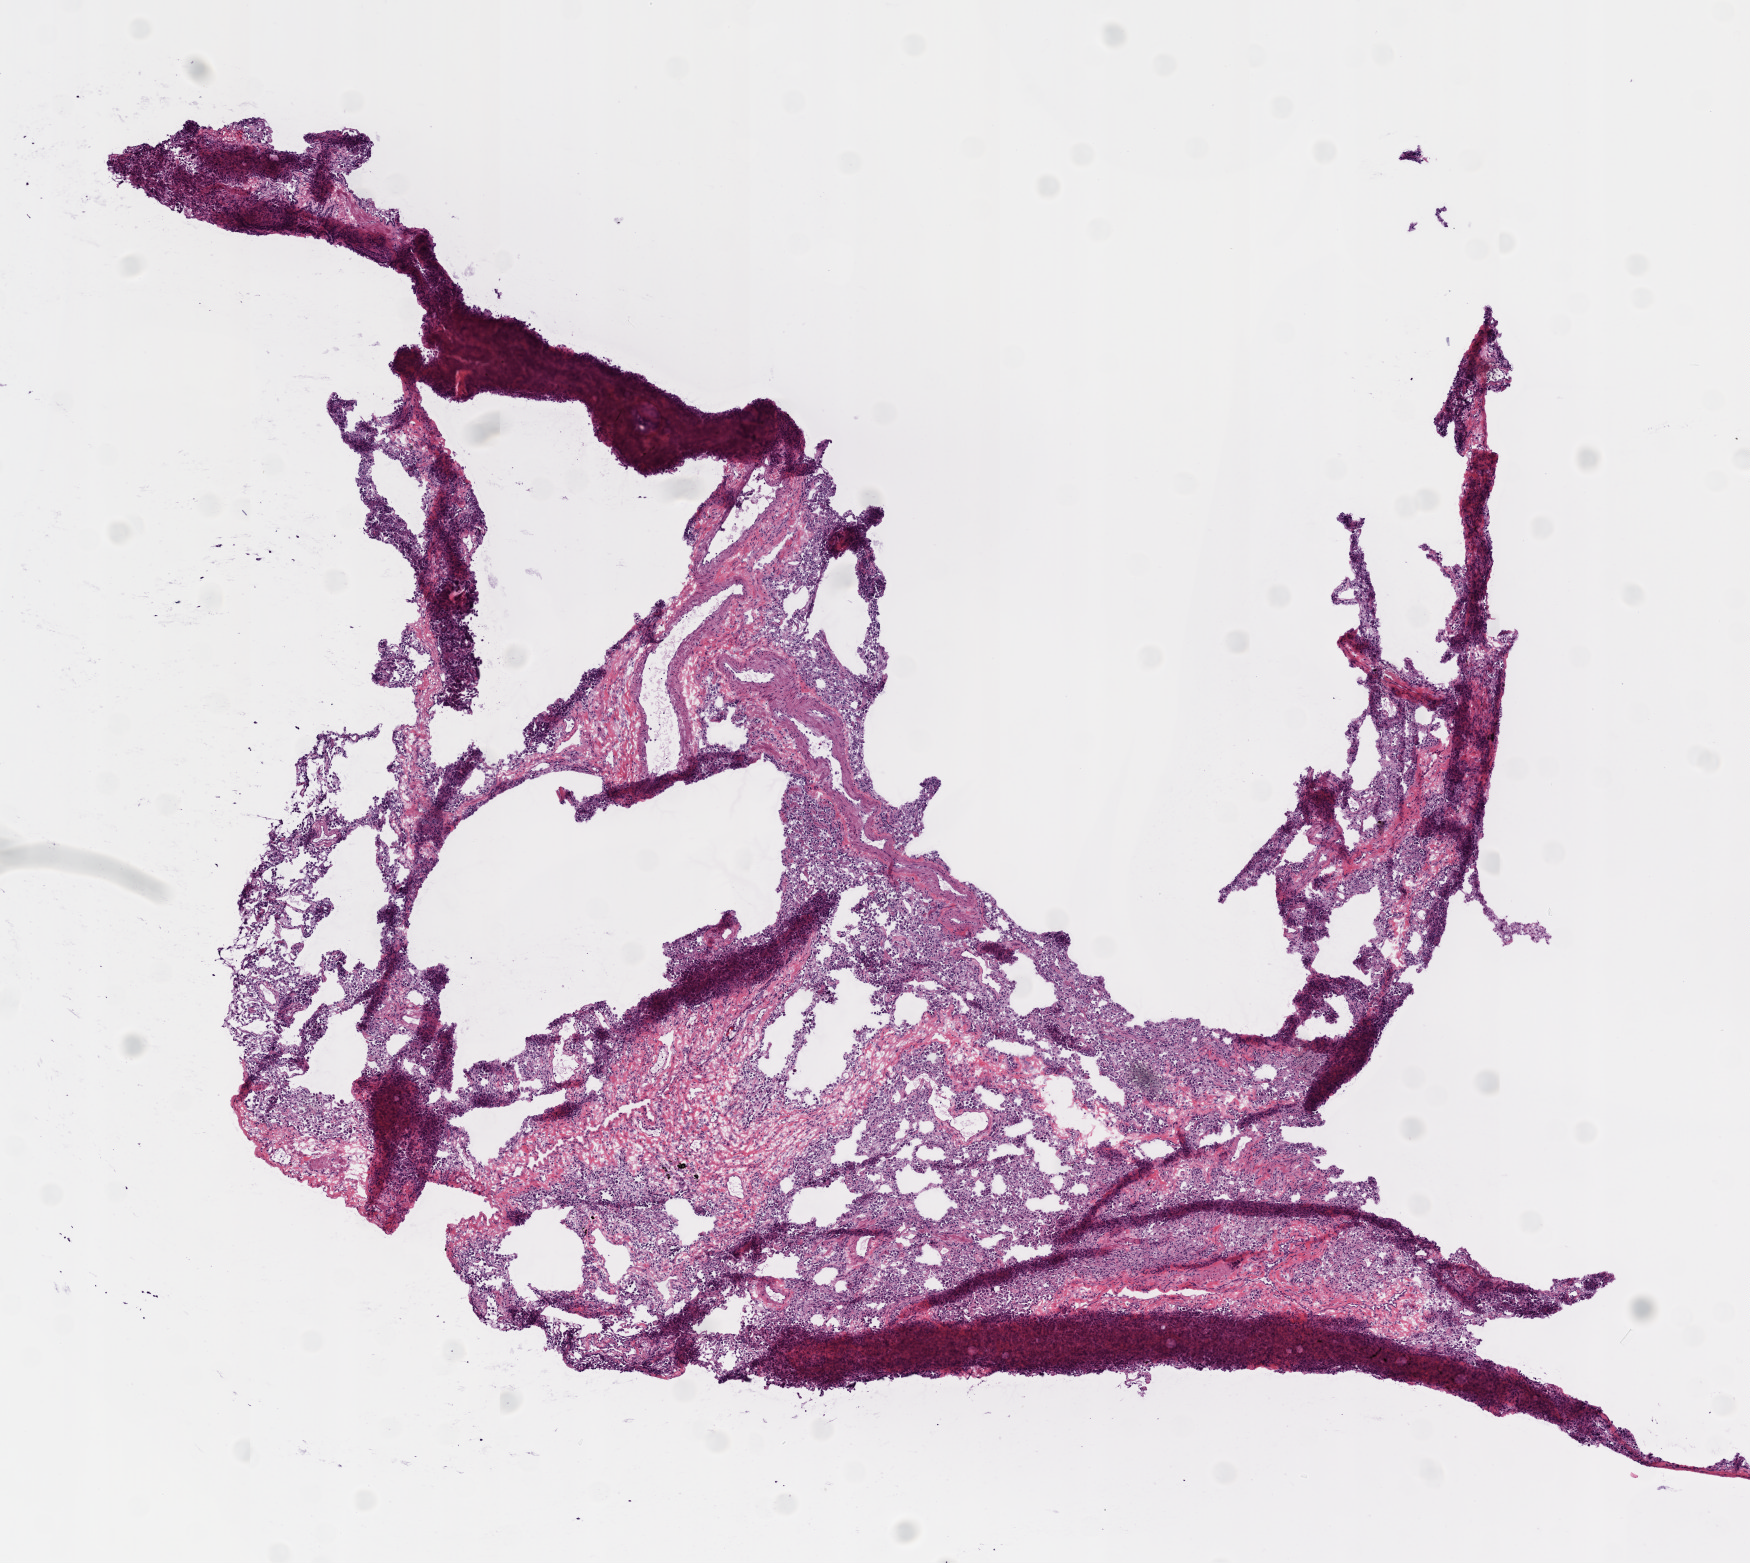
H&E-stained whole-slide image — a low-resolution overview of the entire scanned area, about 7.0 x 6.3 mm. Frozen section from the top of the tissue portion. Solid tissue normal (non-tumour tissue) sample from the lung. Male patient; age at initial diagnosis 72 years.
This section: solid tissue normal (non-tumour) sample from the same patient. Patient diagnosis: Squamous cell carcinoma, NOS (upper lobe, lung).